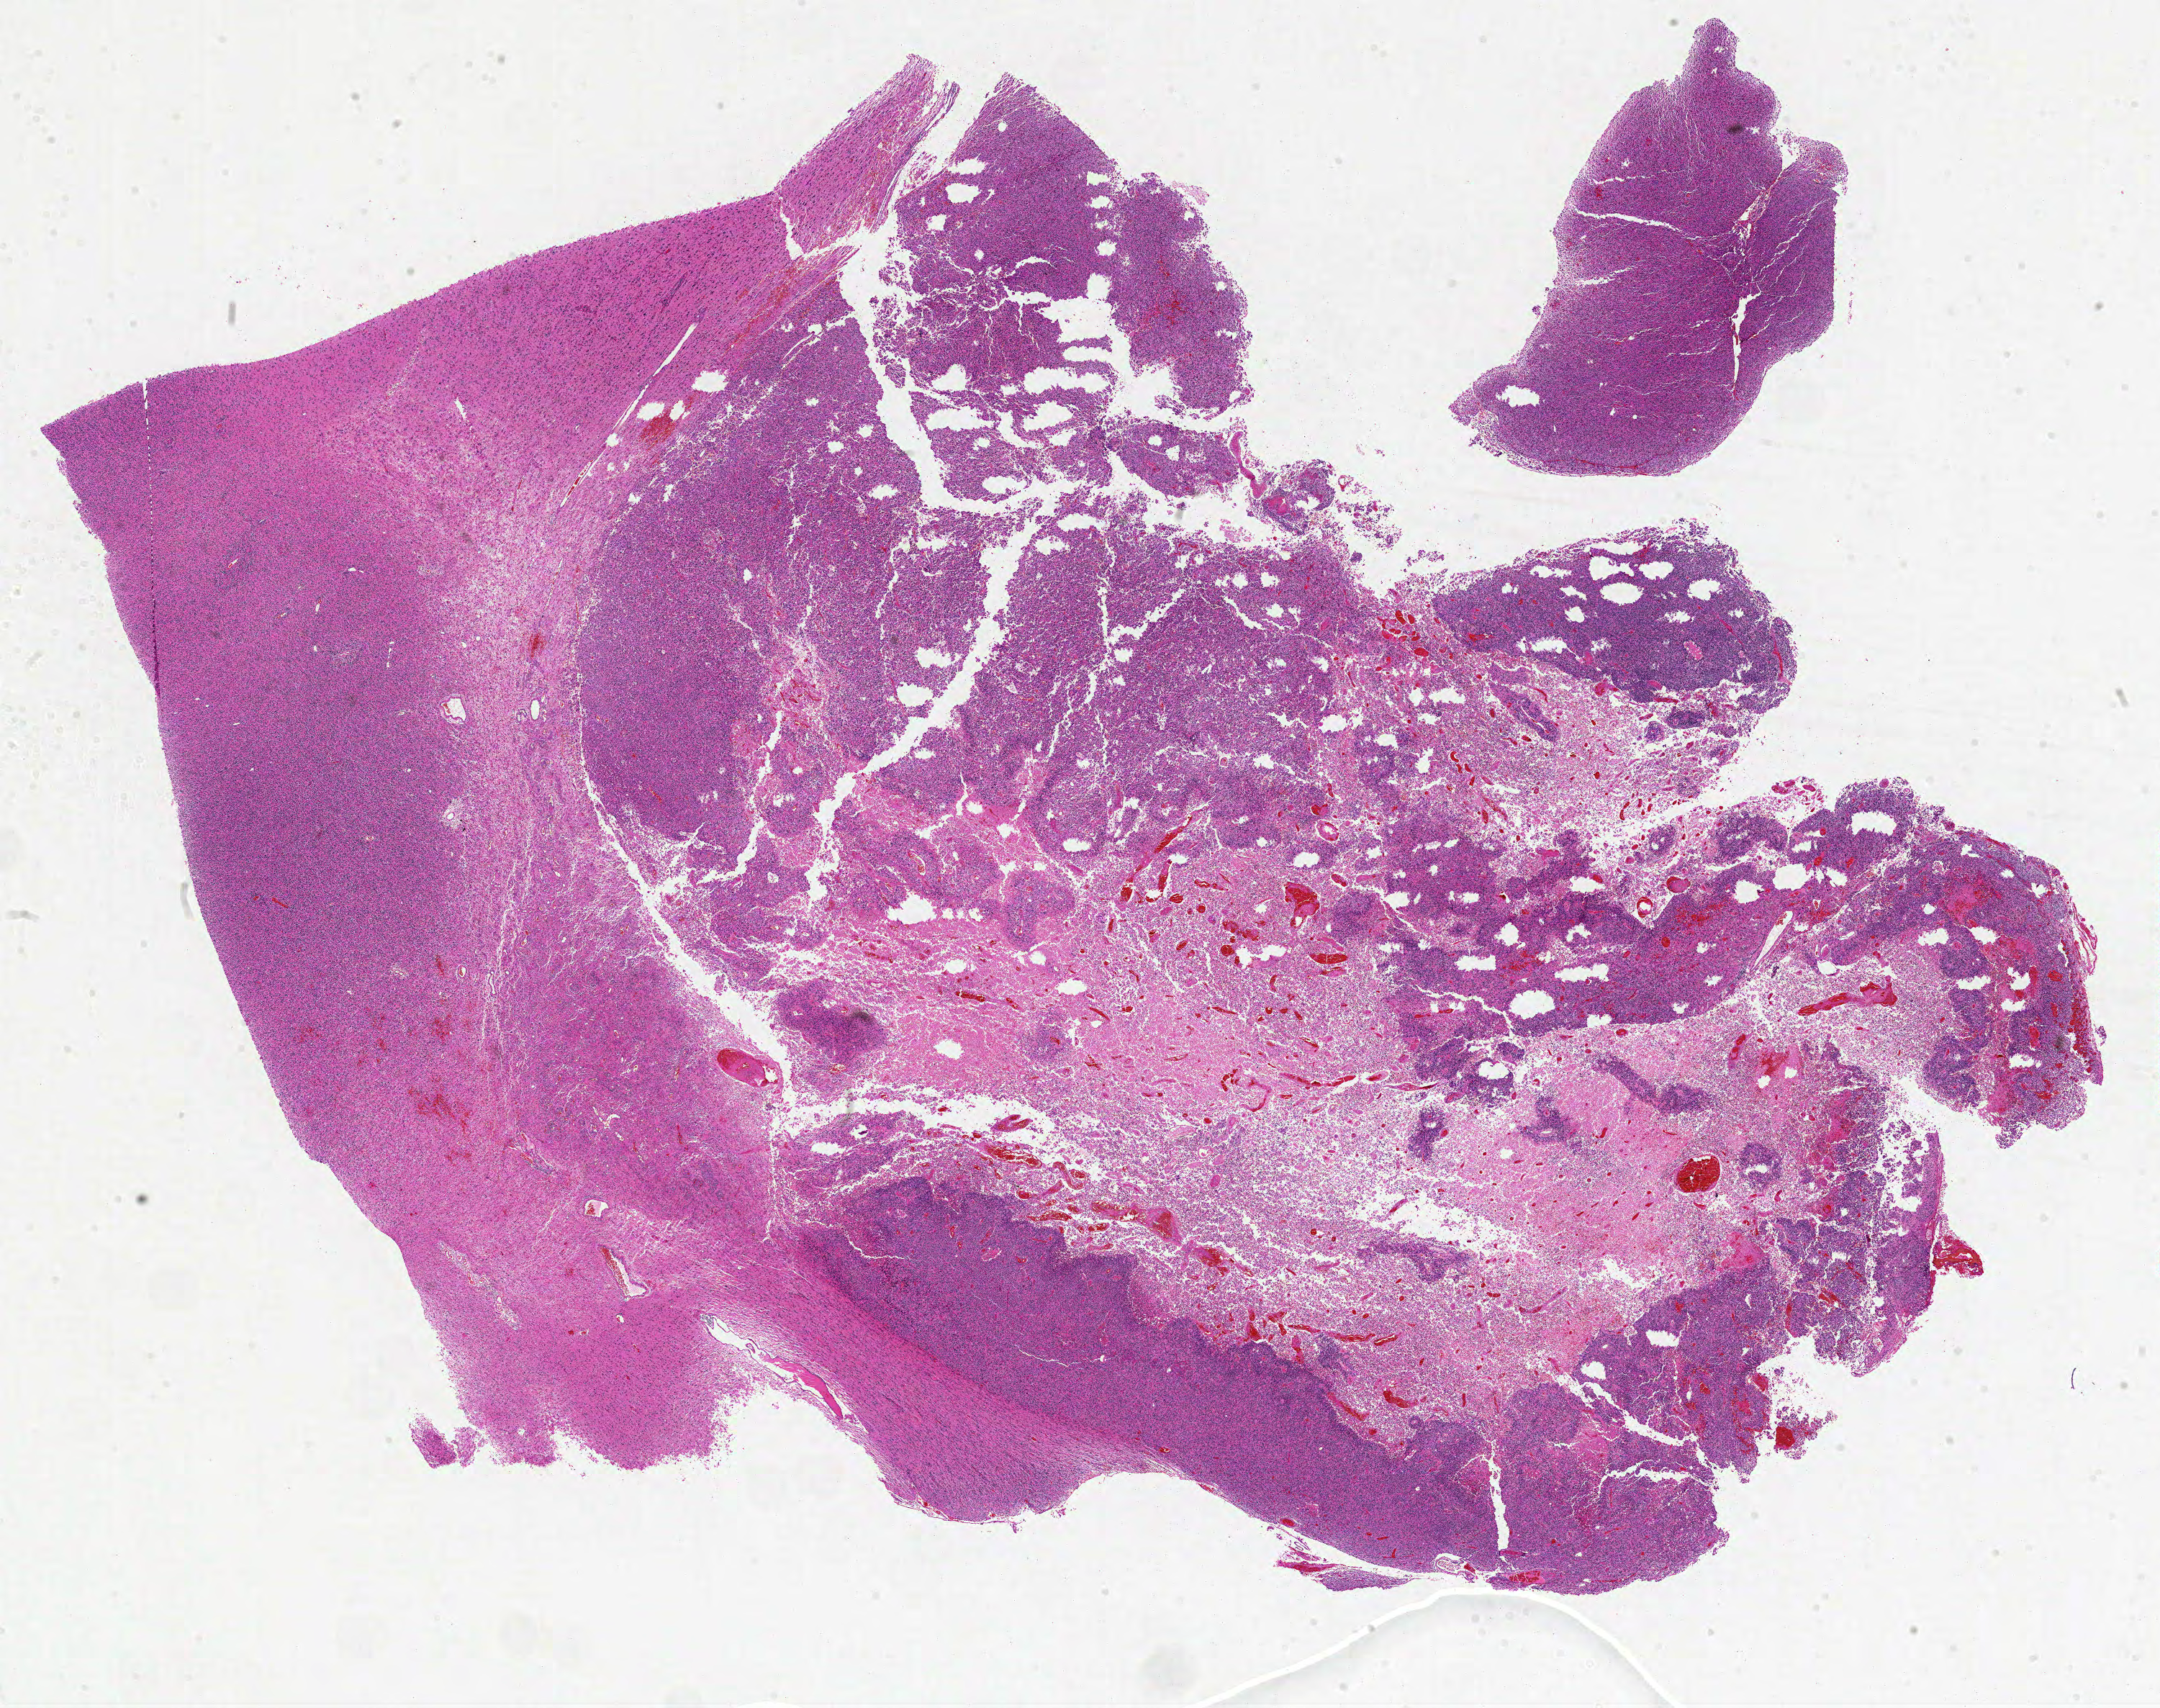
Digitized H&E-stained tissue section (whole slide) — whole scanned area (about 24.0 x 19.0 mm, slide scanned at 20x) shown as a low-resolution overview; FFPE section; sample: primary tumour, brain. Female patient; age at initial diagnosis 34 years.
- pathologic diagnosis: Glioblastoma